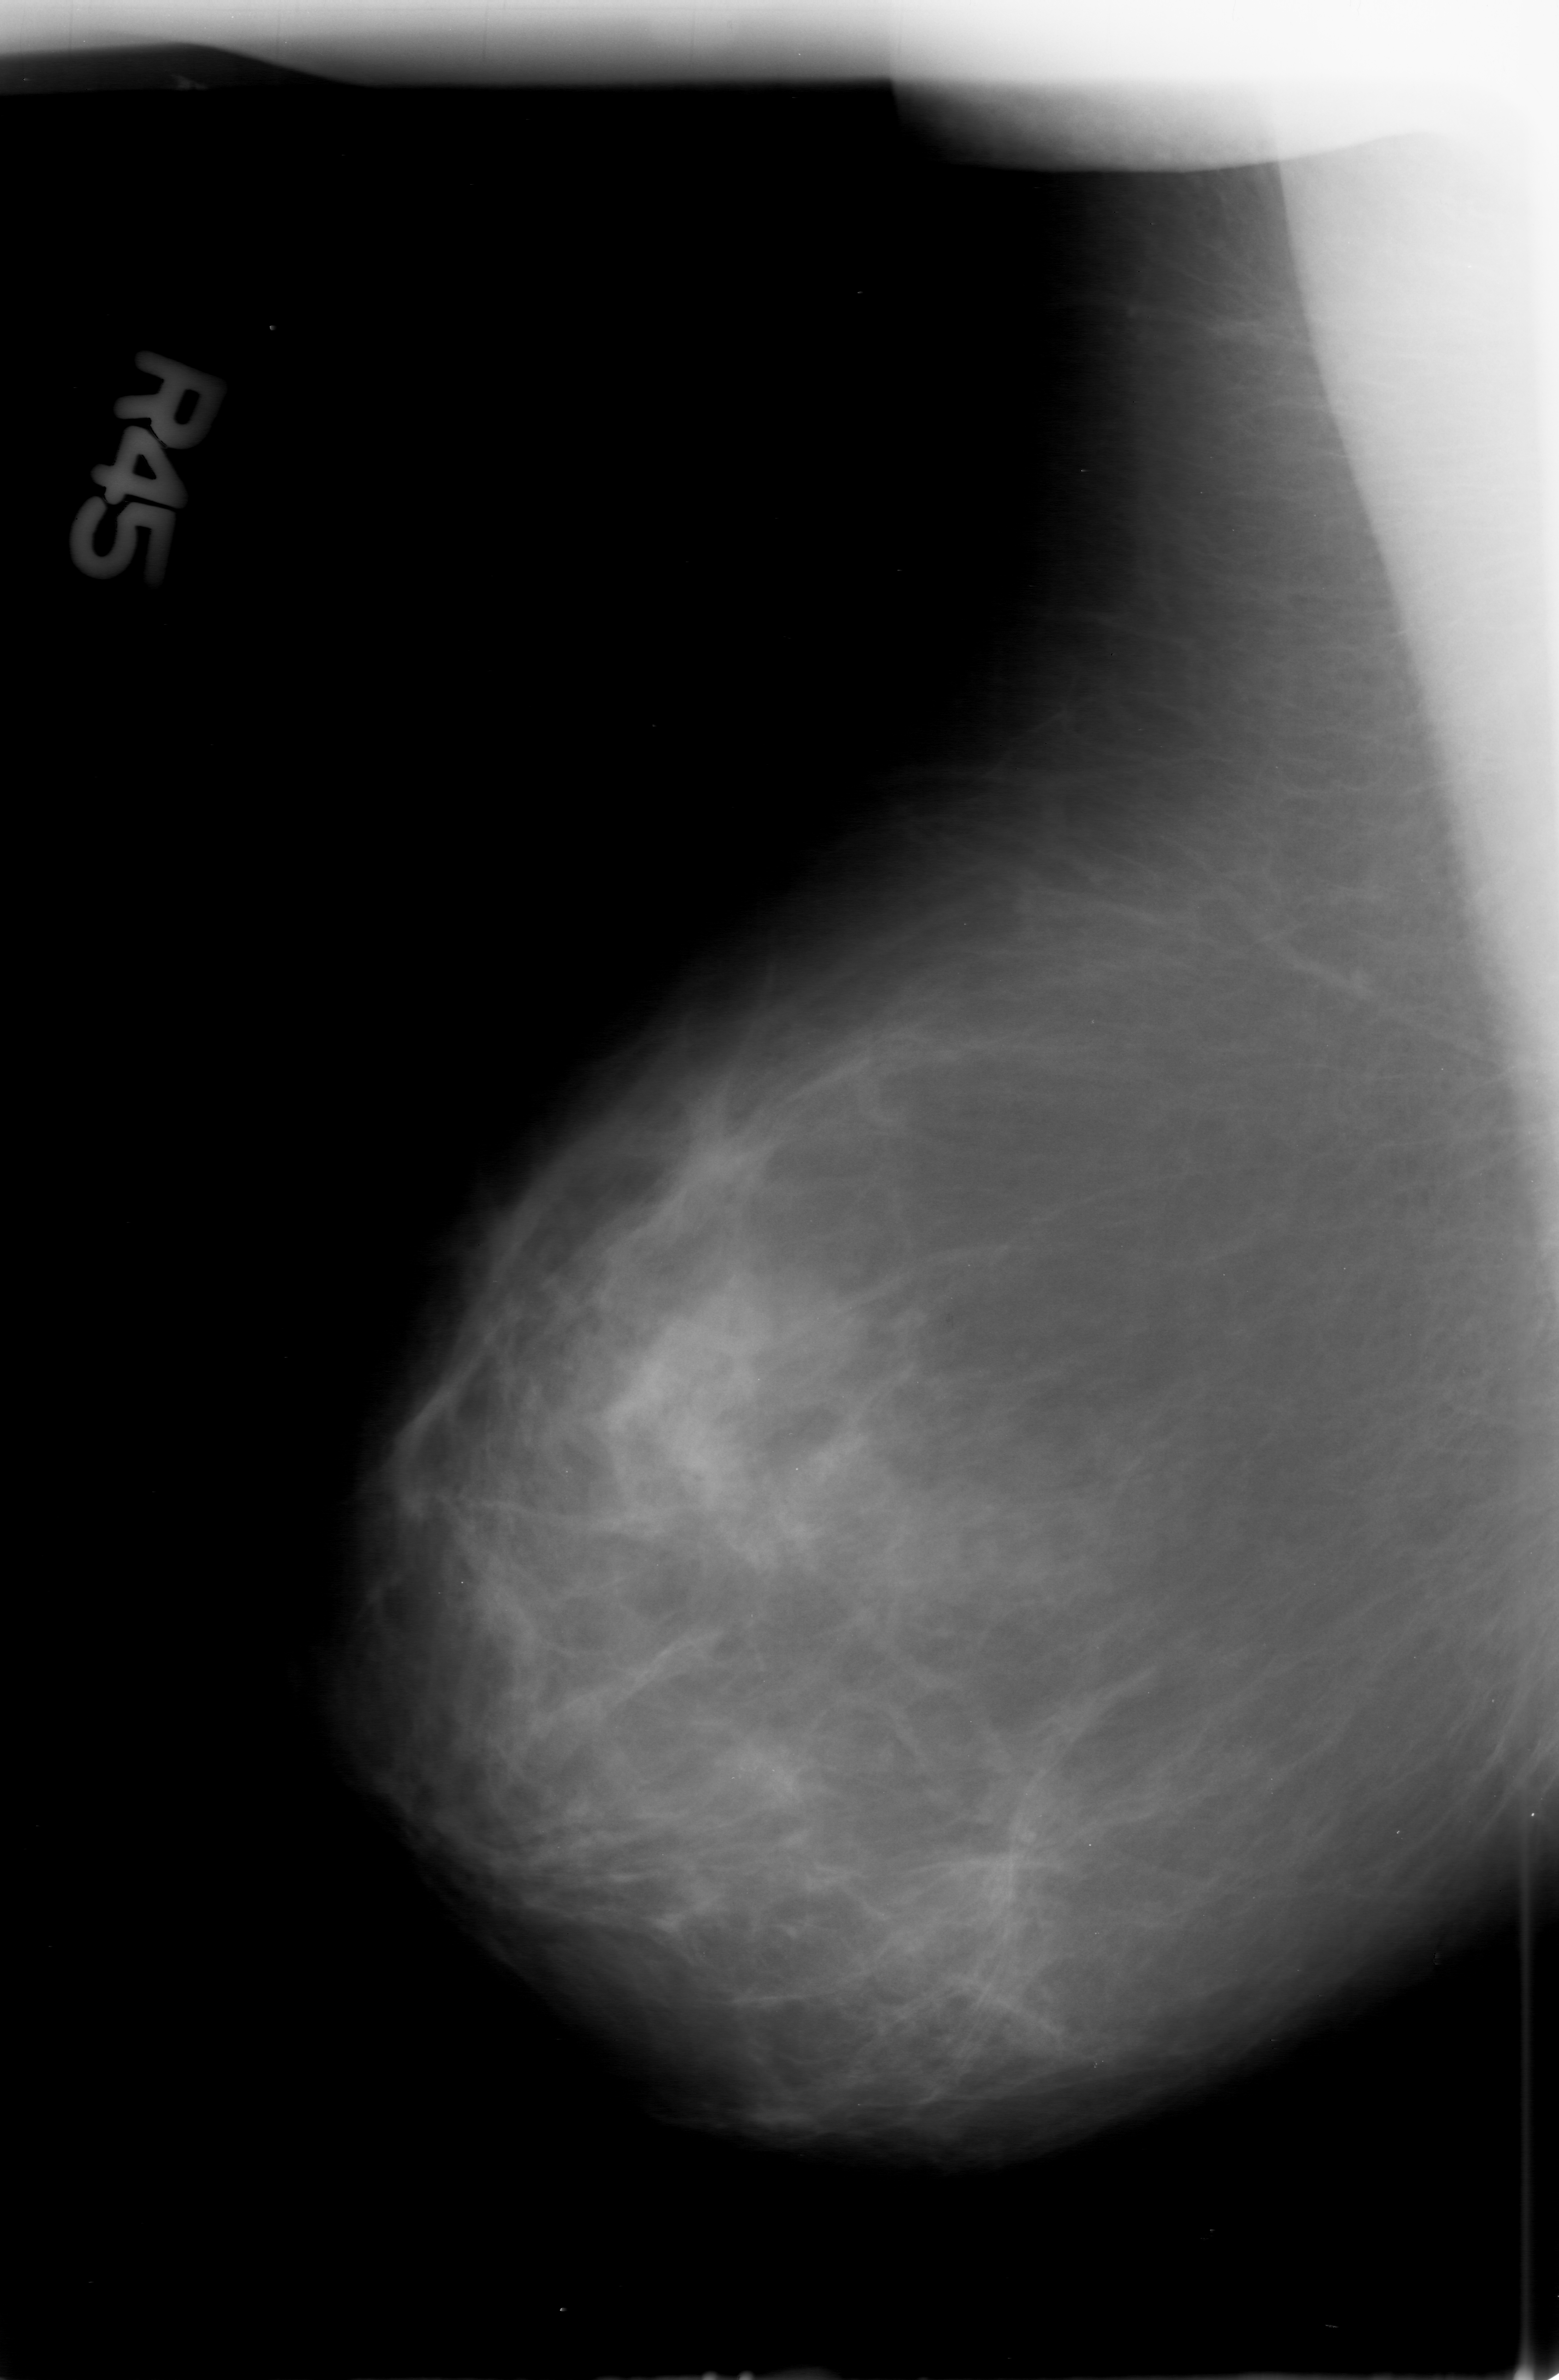
Mammogram (digitized film). Right breast. Mediolateral oblique (MLO) view. BI-RADS breast density category 2 (scale 1–4). 1559 × 2380 image matrix.
Expert-marked regions of interest on this image (one box per marked abnormality):
- calcifications, morphology pleomorphic, distribution clustered; BI-RADS assessment category 0 (incomplete: needs additional imaging); subtlety rating 2 on a 1 (subtle) to 5 (obvious) scale; pathology (as recorded): malignant: bounding box [x1, y1, x2, y2] px = [614, 1610, 1013, 1946]